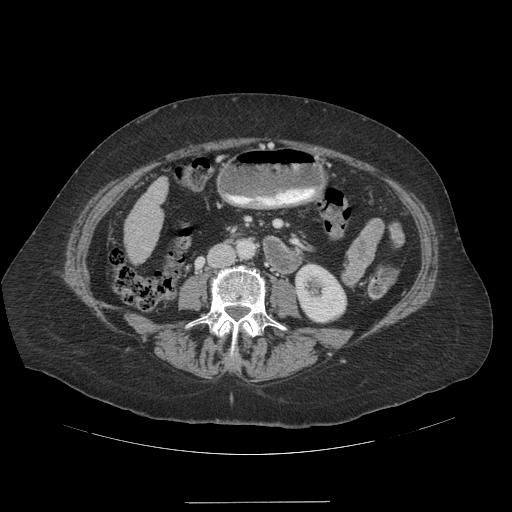
Contrast-enhanced abdominal CT (liver protocol), one axial slice. Reconstruction kernel STANDARD. 140 kVp. Soft-tissue window (W 400 / L 40 HU). 2.5 mm slice thickness. 512 × 512 image matrix, field of view 440 × 440 mm. From the clinical record (not read from this slice): diagnosis: hepatocellular carcinoma (patient treated with transarterial chemoembolisation; whether this scan precedes or follows treatment is not stated here); TNM stage (as recorded): Stage-IVA; Child-Pugh class: A.
Outlined on this slice (semi-automatically segmented with operator editing):
- liver parenchyma outside the tumour (the mass and vessels are separate outlines, so this box may not span the whole liver): bounding box <124,176,168,262> (left, top, right, bottom; pixels)